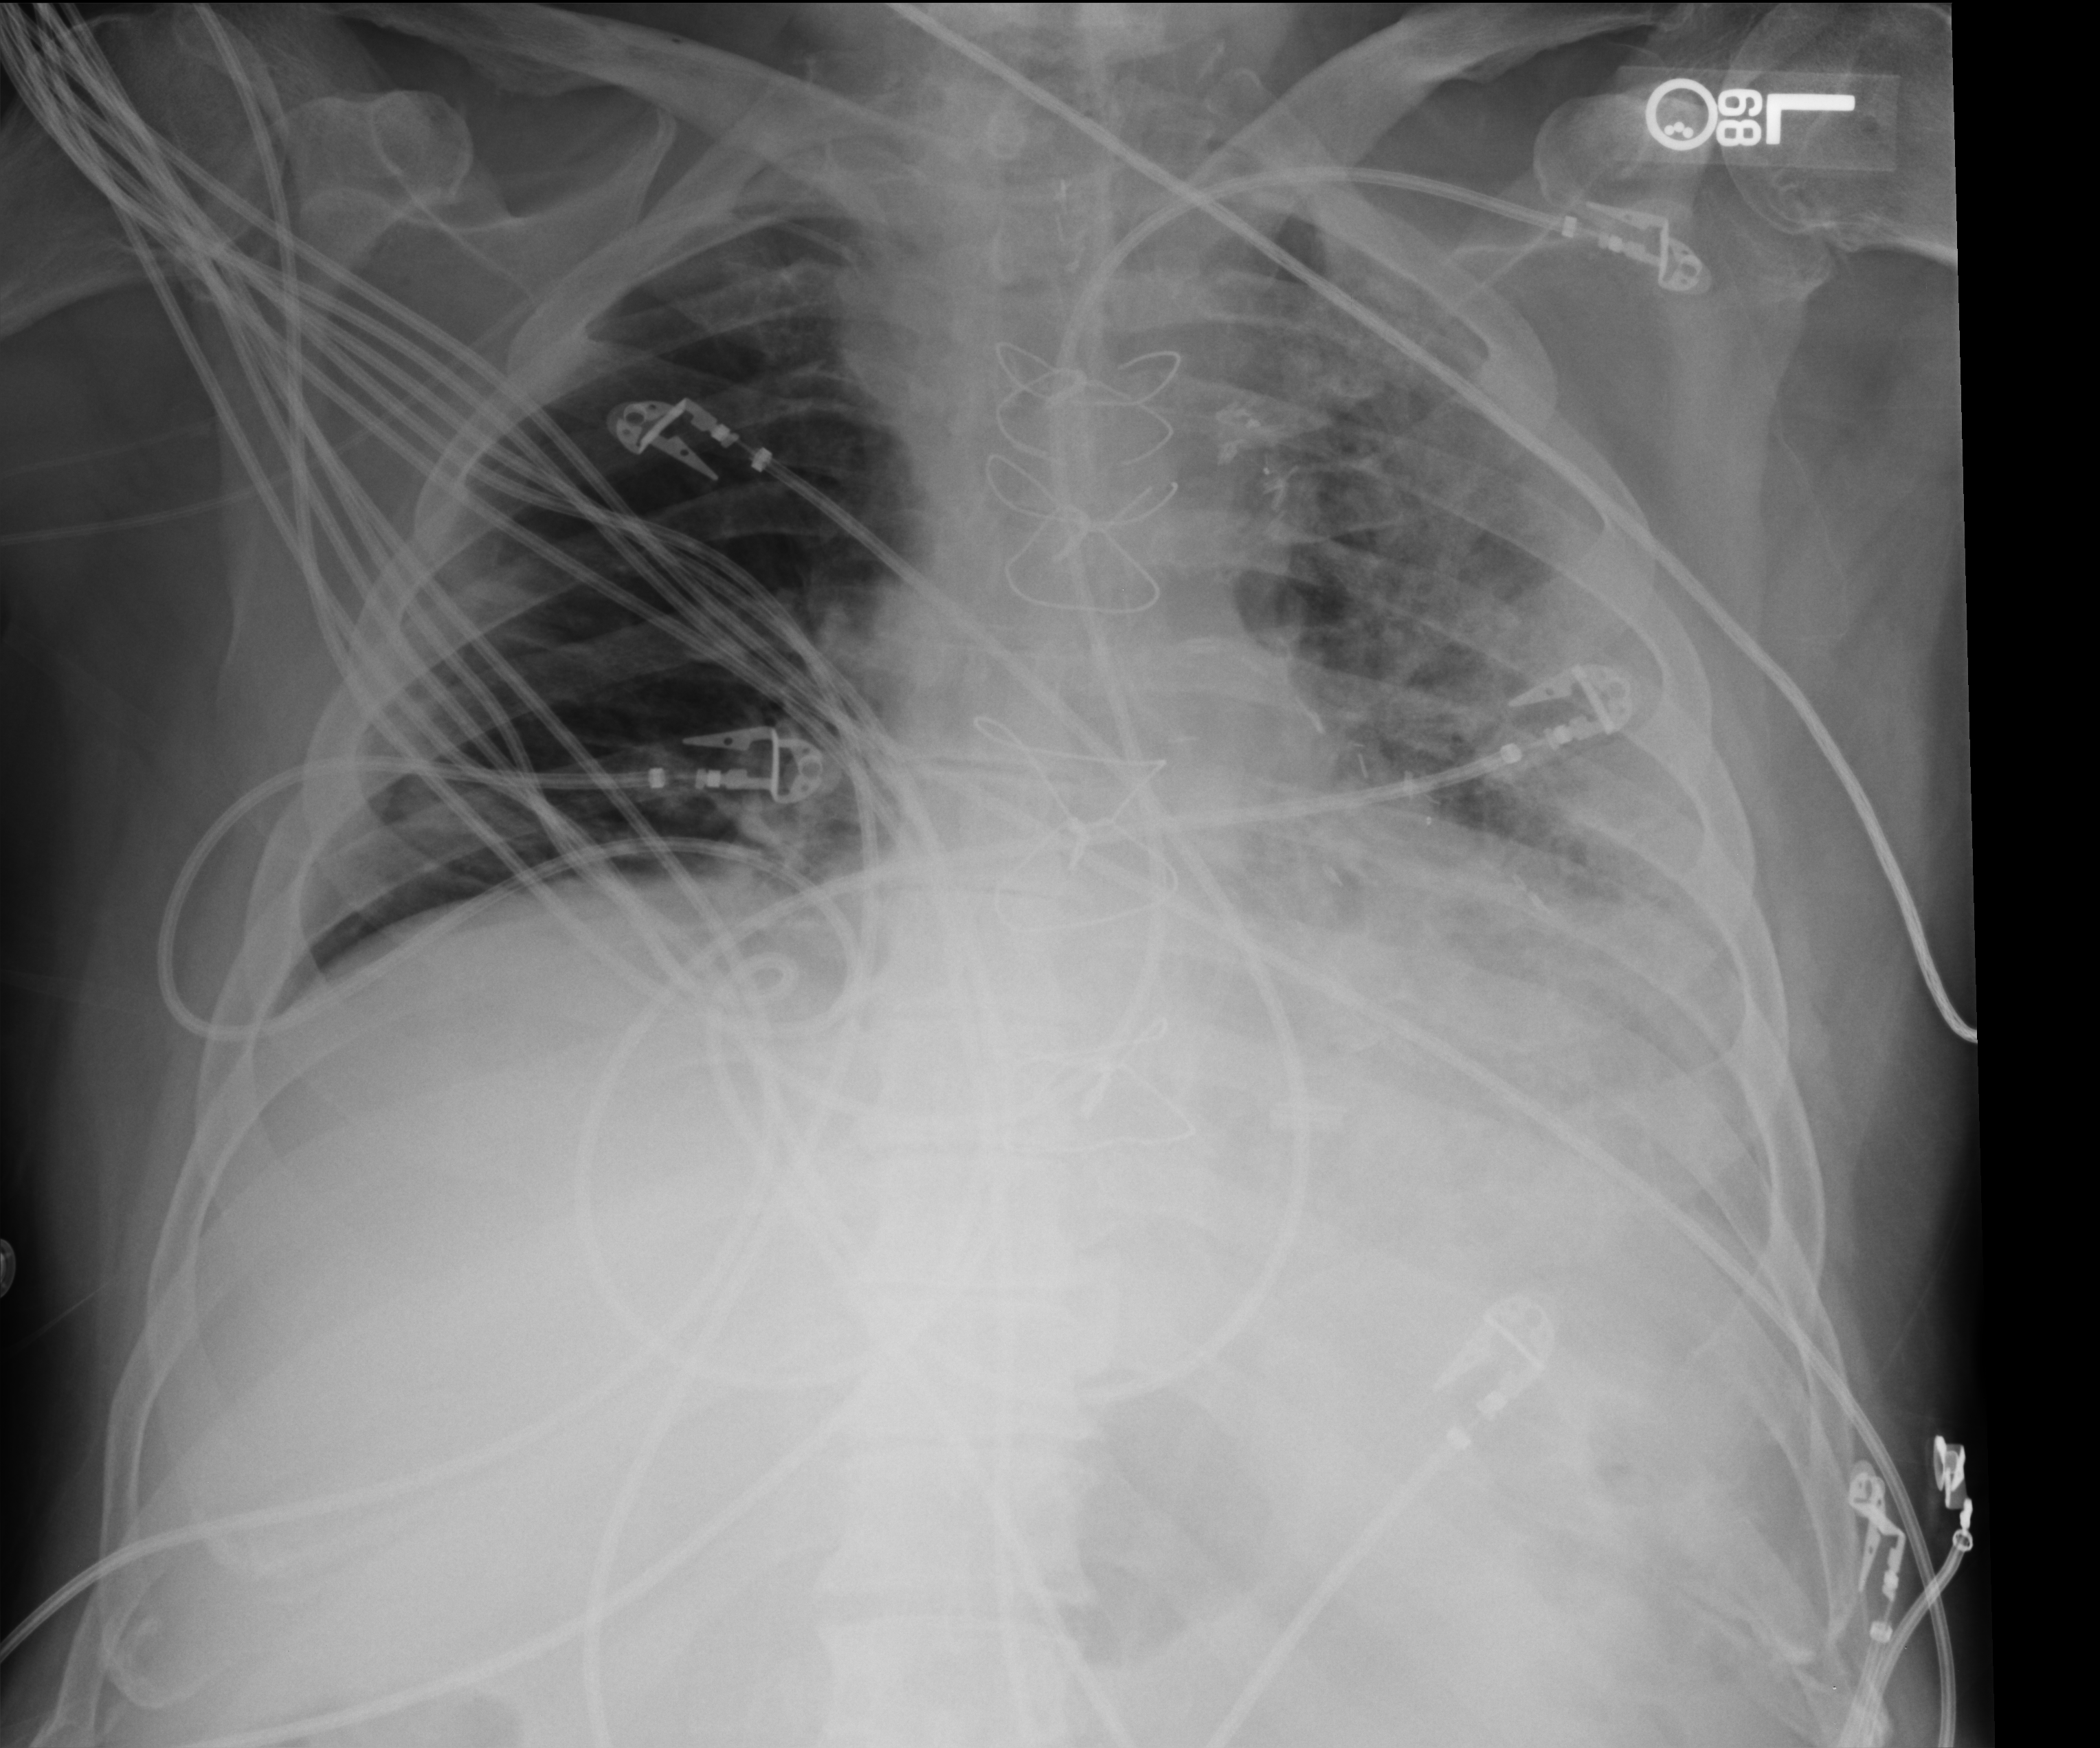
Portable chest radiograph, anteroposterior (AP) projection. Male patient hospitalised with COVID-19, age 60–74 years.
Hospital-stay facts (about this admission, not read from this image; timing relative to this image not recorded):
- mechanically ventilated during this hospital stay: yes